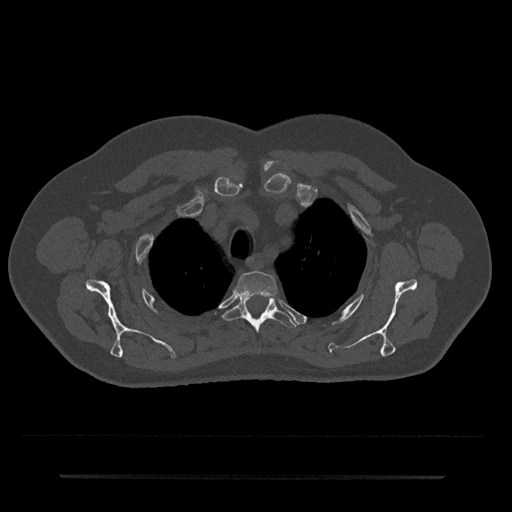
CT including the spine, one axial slice. Slice 579 of 797 in the series (ordered by position). Reconstruction kernel Br40s/3. Bone window (W 1800 / L 400 HU). 0.5 mm slice thickness. 512 × 512 image matrix, field of view 437 × 437 mm. Male patient, age 69 years. From the clinical record (not read from this slice): primary cancer: prostate.
Annotated regions visible in this slice (semi-automatic segmentation, software-assisted and operator-edited):
- T2 vertebra: box from (x=235, y=271) to (x=277, y=296) px
- T3 vertebra: (x=223, y=296)–(x=297, y=333)